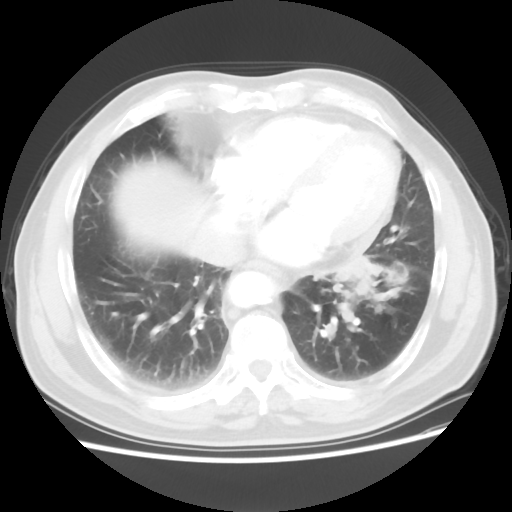
Chest CT, one axial slice. Position 22 of 56 along the scan axis. 120 kVp. Lung window (W 1500 / L -600 HU). 5 mm slice thickness. 512 × 512 image matrix, field of view 360 × 360 mm. Patient: male, 75 years. Case-level facts recorded for this patient, not image findings: clinical TNM (as recorded): T3 N0 M0.
Outlined on this slice (rectangle marked by the reading radiologist):
- lung tumour (recorded histology: squamous cell carcinoma): bounding box [x1, y1, x2, y2] px = [328, 242, 403, 304]